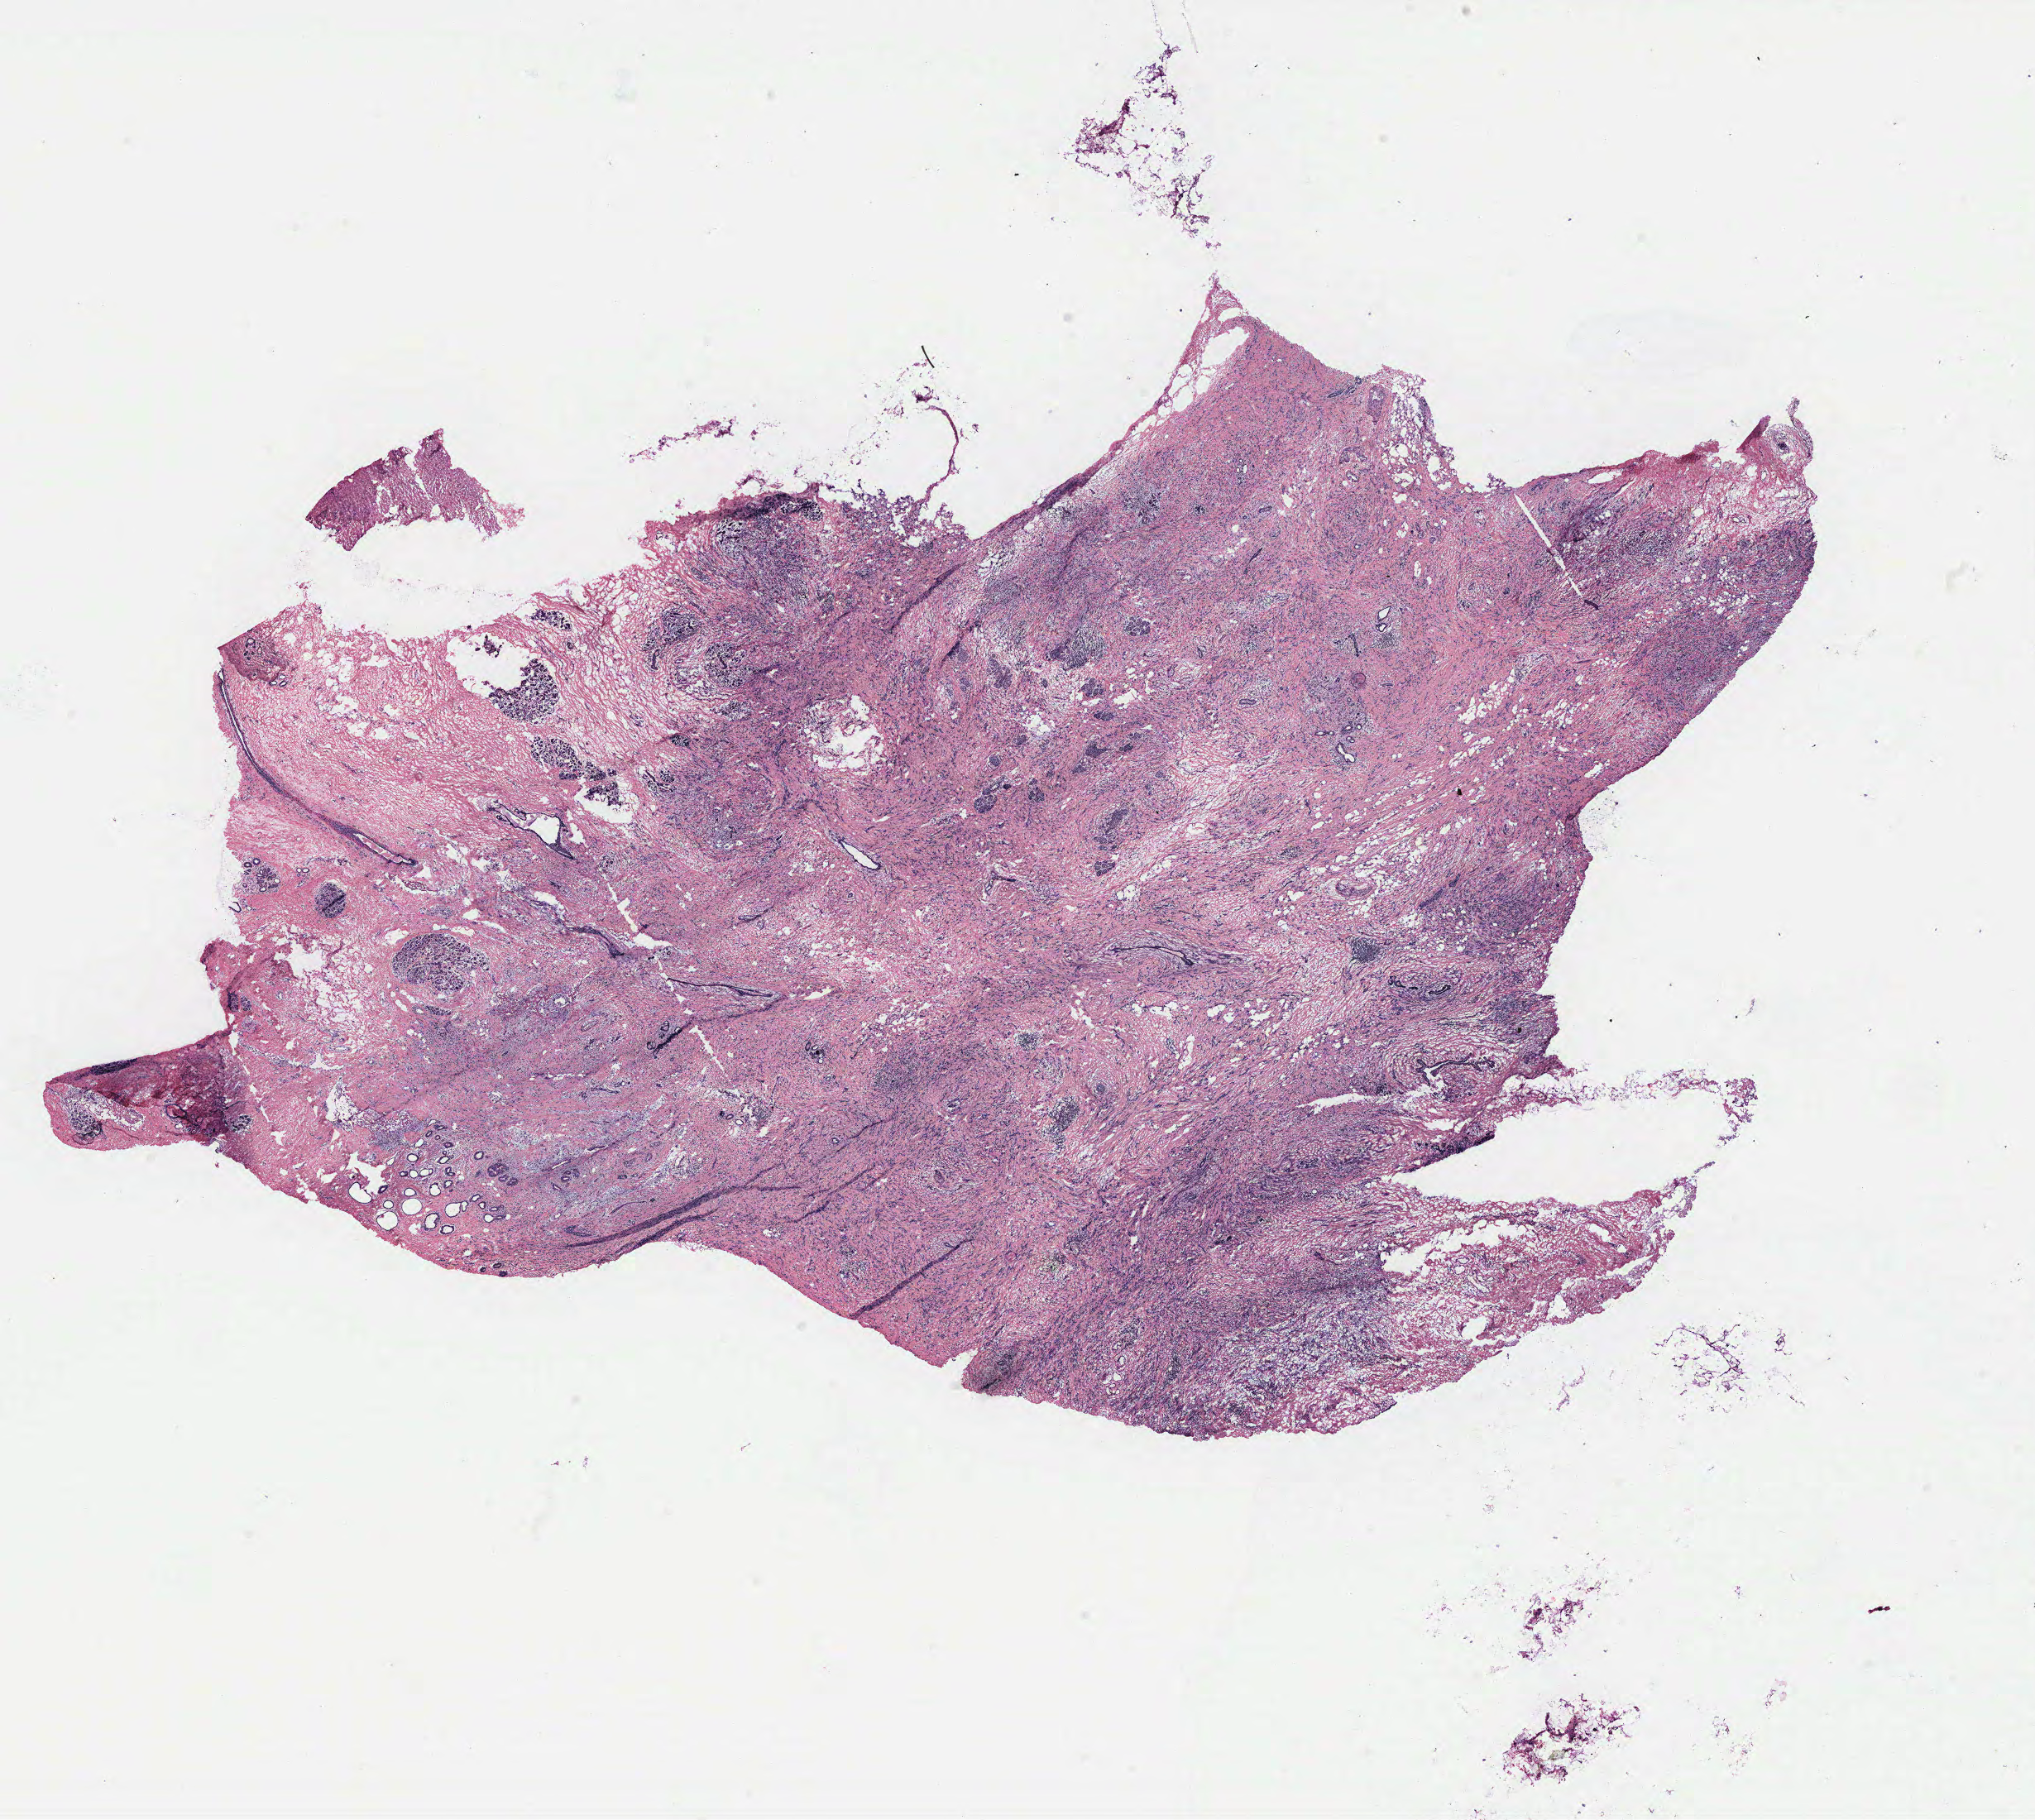
Hematoxylin and eosin (H&E) stained whole-slide image — a low-resolution overview of the entire scanned area, about 19.7 x 17.6 mm (slide scanned at 40x). Breast, tumour tissue. Female, 54 y/o.
Histologic diagnosis: Infiltrating lobular carcinoma, NOS. AJCC pathologic stage: IIIA.